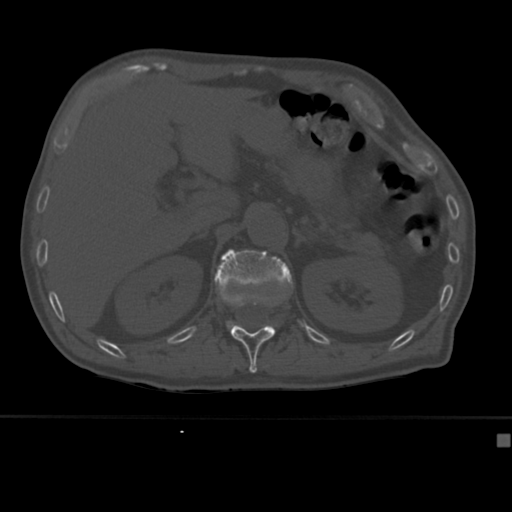
CT including the spine, one axial slice; slice 183 of 430 in the series (ordered by position); reconstruction kernel Br40s; 120 kVp; bone window (W 1800 / L 400 HU); 1.5 mm slice thickness; 512 × 512 image matrix, field of view 337 × 337 mm. Patient: male, 64 years. From the clinical record (not read from this slice): primary cancer: uterus.
Outlined on this slice (semi-automatic segmentation, software-assisted and operator-edited):
- L1 vertebra: bounding box <214,249,293,332> (left, top, right, bottom; pixels)
- T12 vertebra: <231,305,275,373>